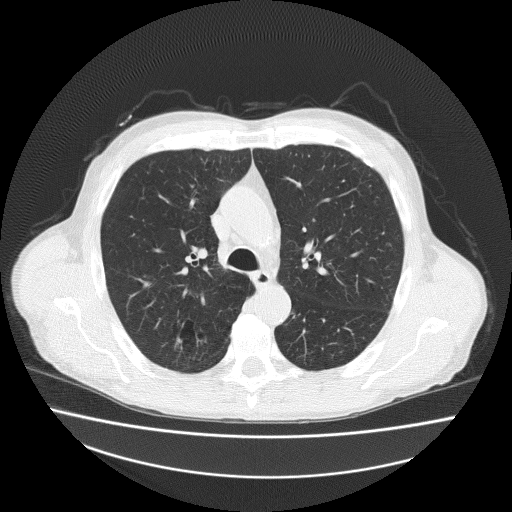
Low-dose screening chest CT, axial slice, second annual screen, lung window (W 1500 / L -600 HU), 2 mm slice thickness, lung (sharp) reconstruction kernel (FC51), 120 kVp, slice 68 of 186 in the series, 512 × 512 image matrix, field of view 408 × 408 mm. Male participant, aged 73 years at enrolment. Current smoker at enrolment.
Expert-annotated lung lesion, bounding box (x1, y1, x2, y2) in pixels: (162, 315, 217, 361). Screening reader's record for this exam: no non-calcified nodule ≥4 mm recorded. Official screen result: negative screen, minor abnormalities not suspicious for lung cancer. Participant outcome: lung cancer diagnosed 418 days after this screen (after the third annual screen) — adenosquamous carcinoma, right upper lobe, well differentiated (G1), stage IA (AJCC 6th edition), 20 mm at pathology.